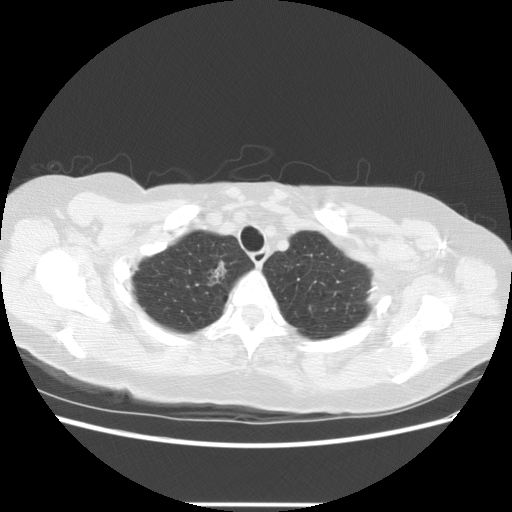
Low-dose screening chest CT, one axial slice. Position 110 of 126 along the scan axis. Reconstruction kernel STANDARD. Lung window (W 1500 / L -600 HU). 2.5 mm slice thickness. 512 × 512 image matrix, field of view 360 × 360 mm.
Outlined on this slice (outlined manually by an expert reader):
- lesion 1 (tumor, upper lobe of right lung): bounding box <207,261,227,286> (left, top, right, bottom; pixels)